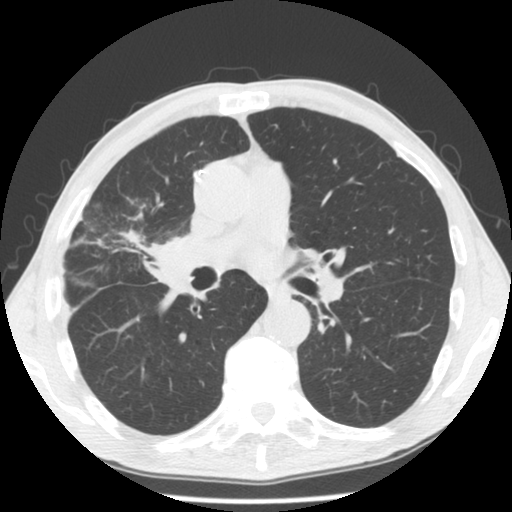
Chest CT (low-dose screening protocol), one axial image. Third annual screen. Lung window (W 1500 / L -600 HU). 2.5 mm slice thickness. 140 kVp. Slice 73 of 132 in the series. Male, age 57 years at enrolment. Former smoker at enrolment.
Expert-annotated lung lesion, bounding box (x1, y1, x2, y2) in pixels: (54, 195, 167, 292). Reader record for this screening exam (exam-level; its link to the box is not recorded): non-calcified nodule or mass ≥4 mm, right upper lobe, 38 × 34 mm, poorly defined margins, mixed attenuation, pre-existing on the prior screen: no.